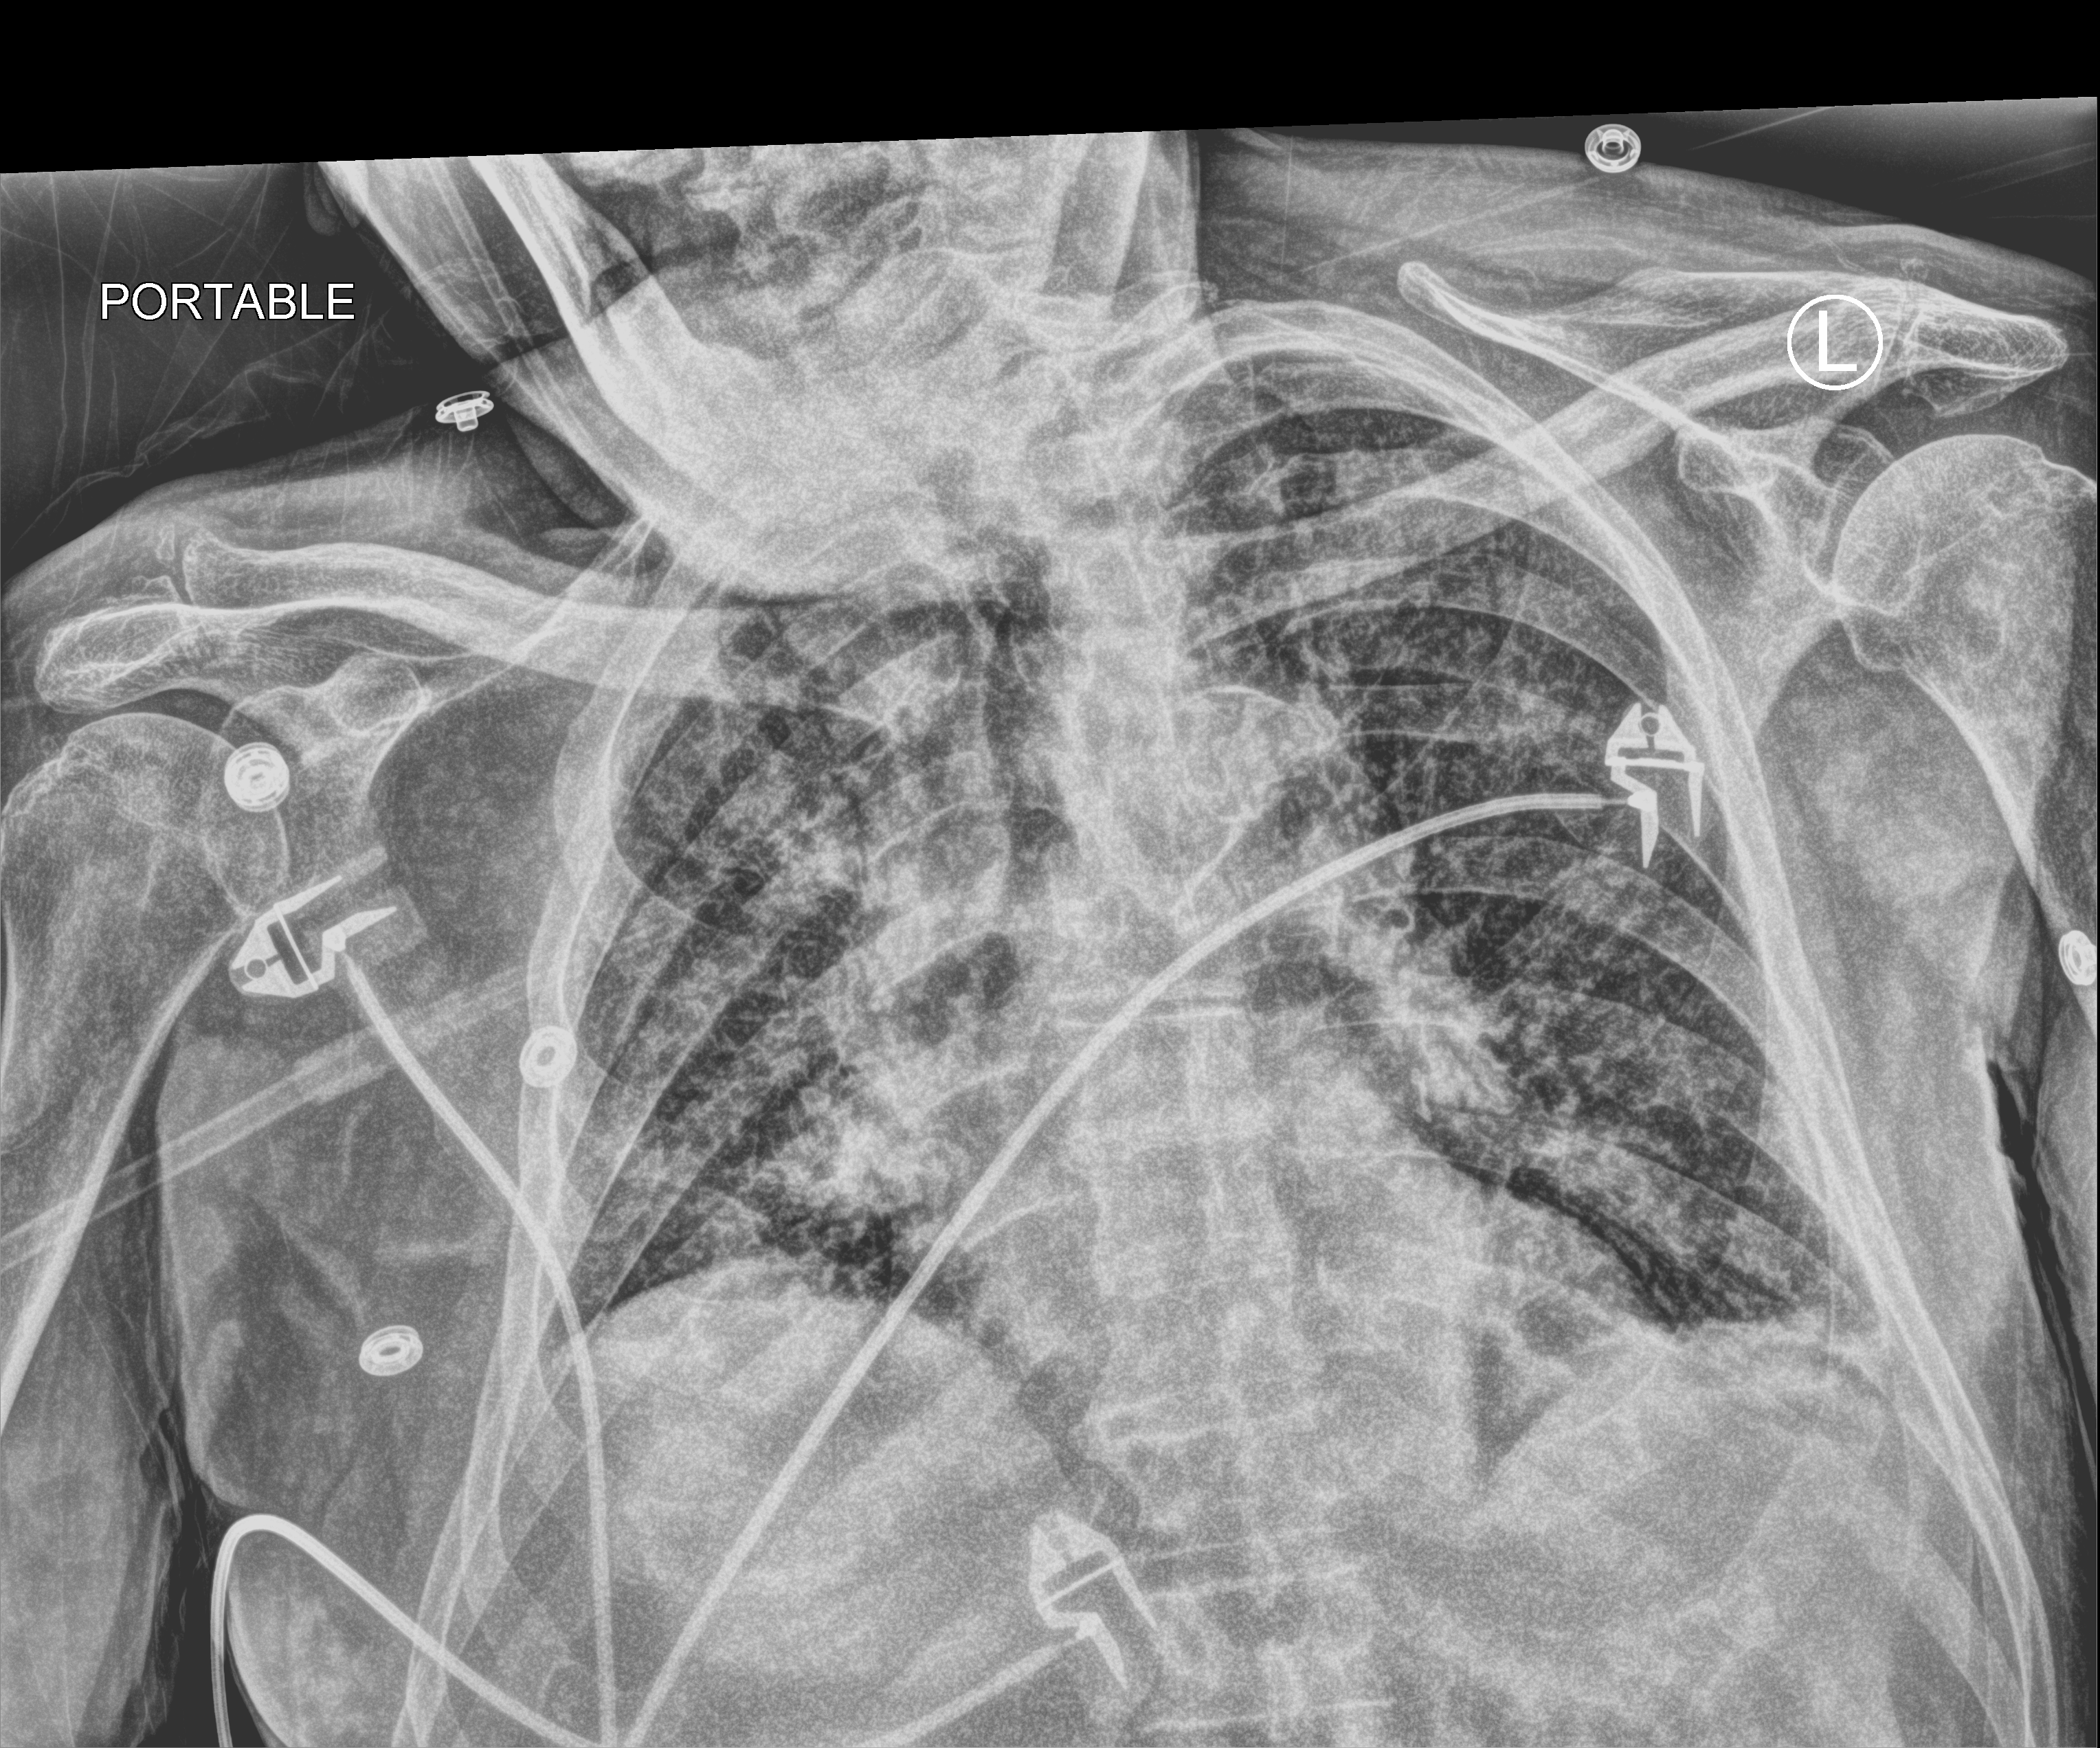
Portable chest radiograph, anteroposterior (AP) projection. Patient hospitalised with COVID-19; male, aged 75–90 years.
From the hospital-stay record, not from the radiograph (when in the stay this image was taken is not recorded): mechanically ventilated during this hospital stay: yes; admitted to intensive care during this hospital stay: yes; smoking status (admission record): never.